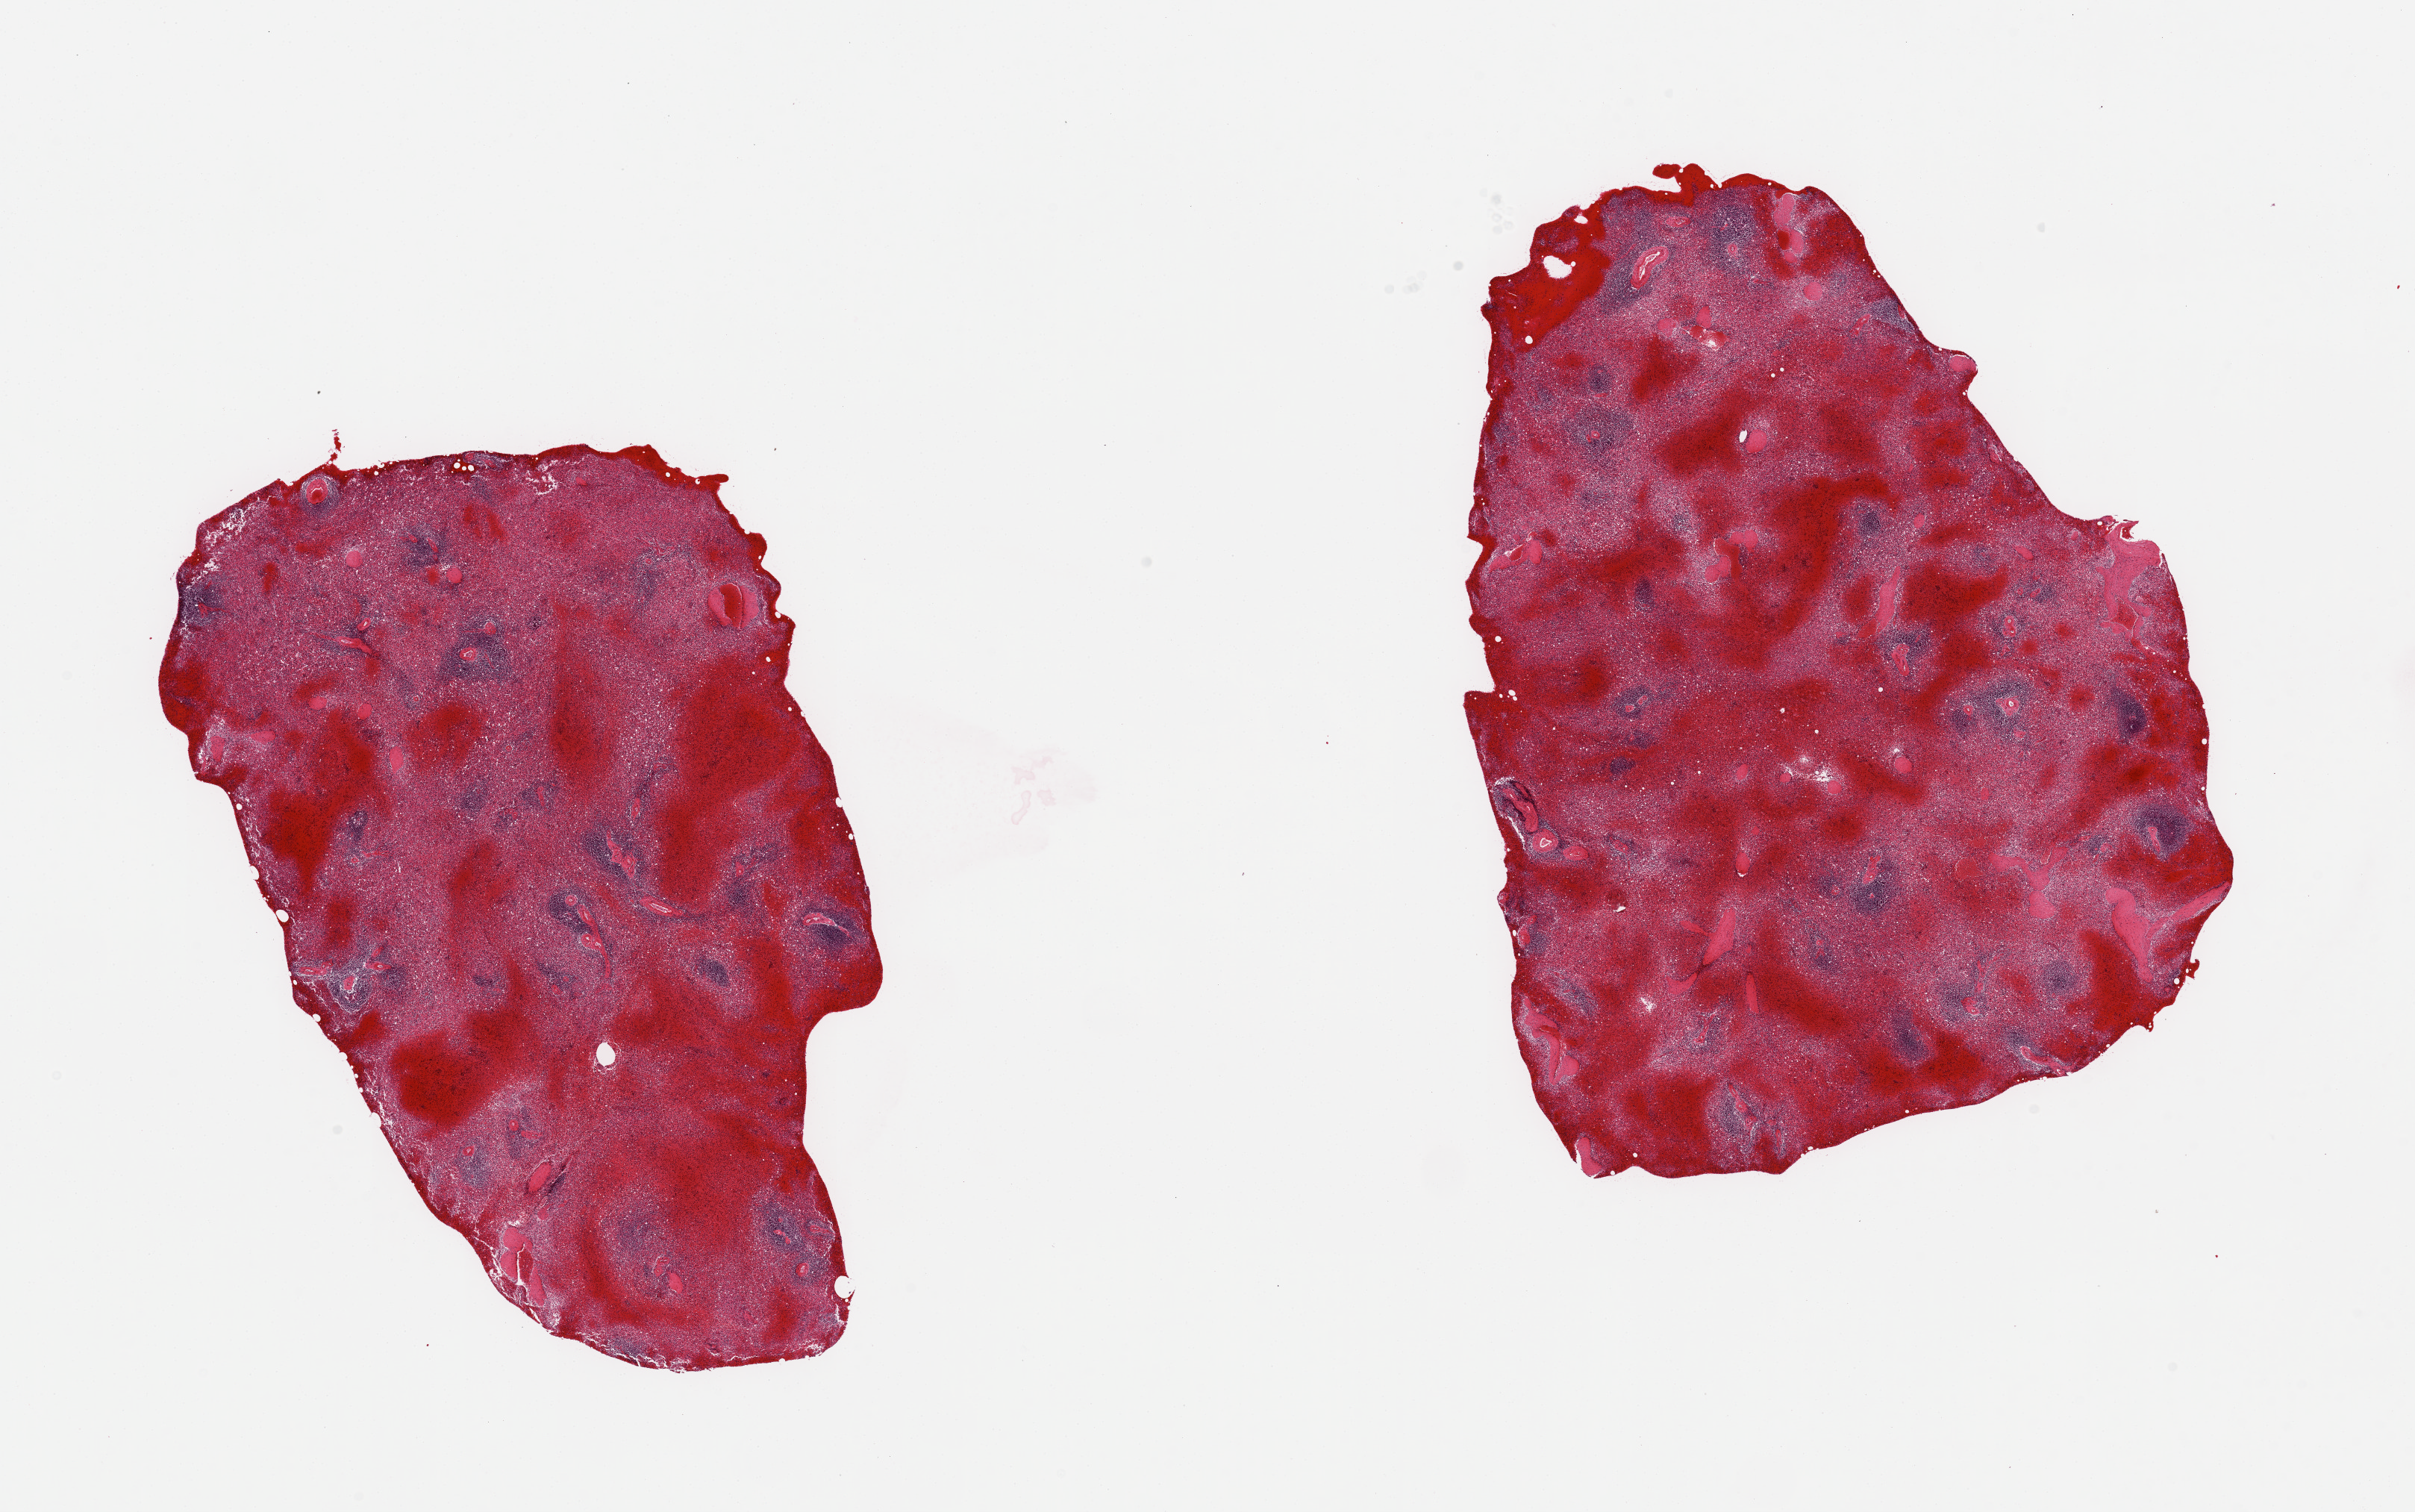
H&E whole-slide image, brightfield — low-resolution overview of the scanned area, about 25.6 x 16.0 mm; PAXgene-fixed paraffin-embedded (PFPE) section; sampled site (target tissue): spleen; donor tissue sample. Male donor.
Reviewer comment on this tissue sample: 2 pieces, marked congestion, markedly autolyzed.